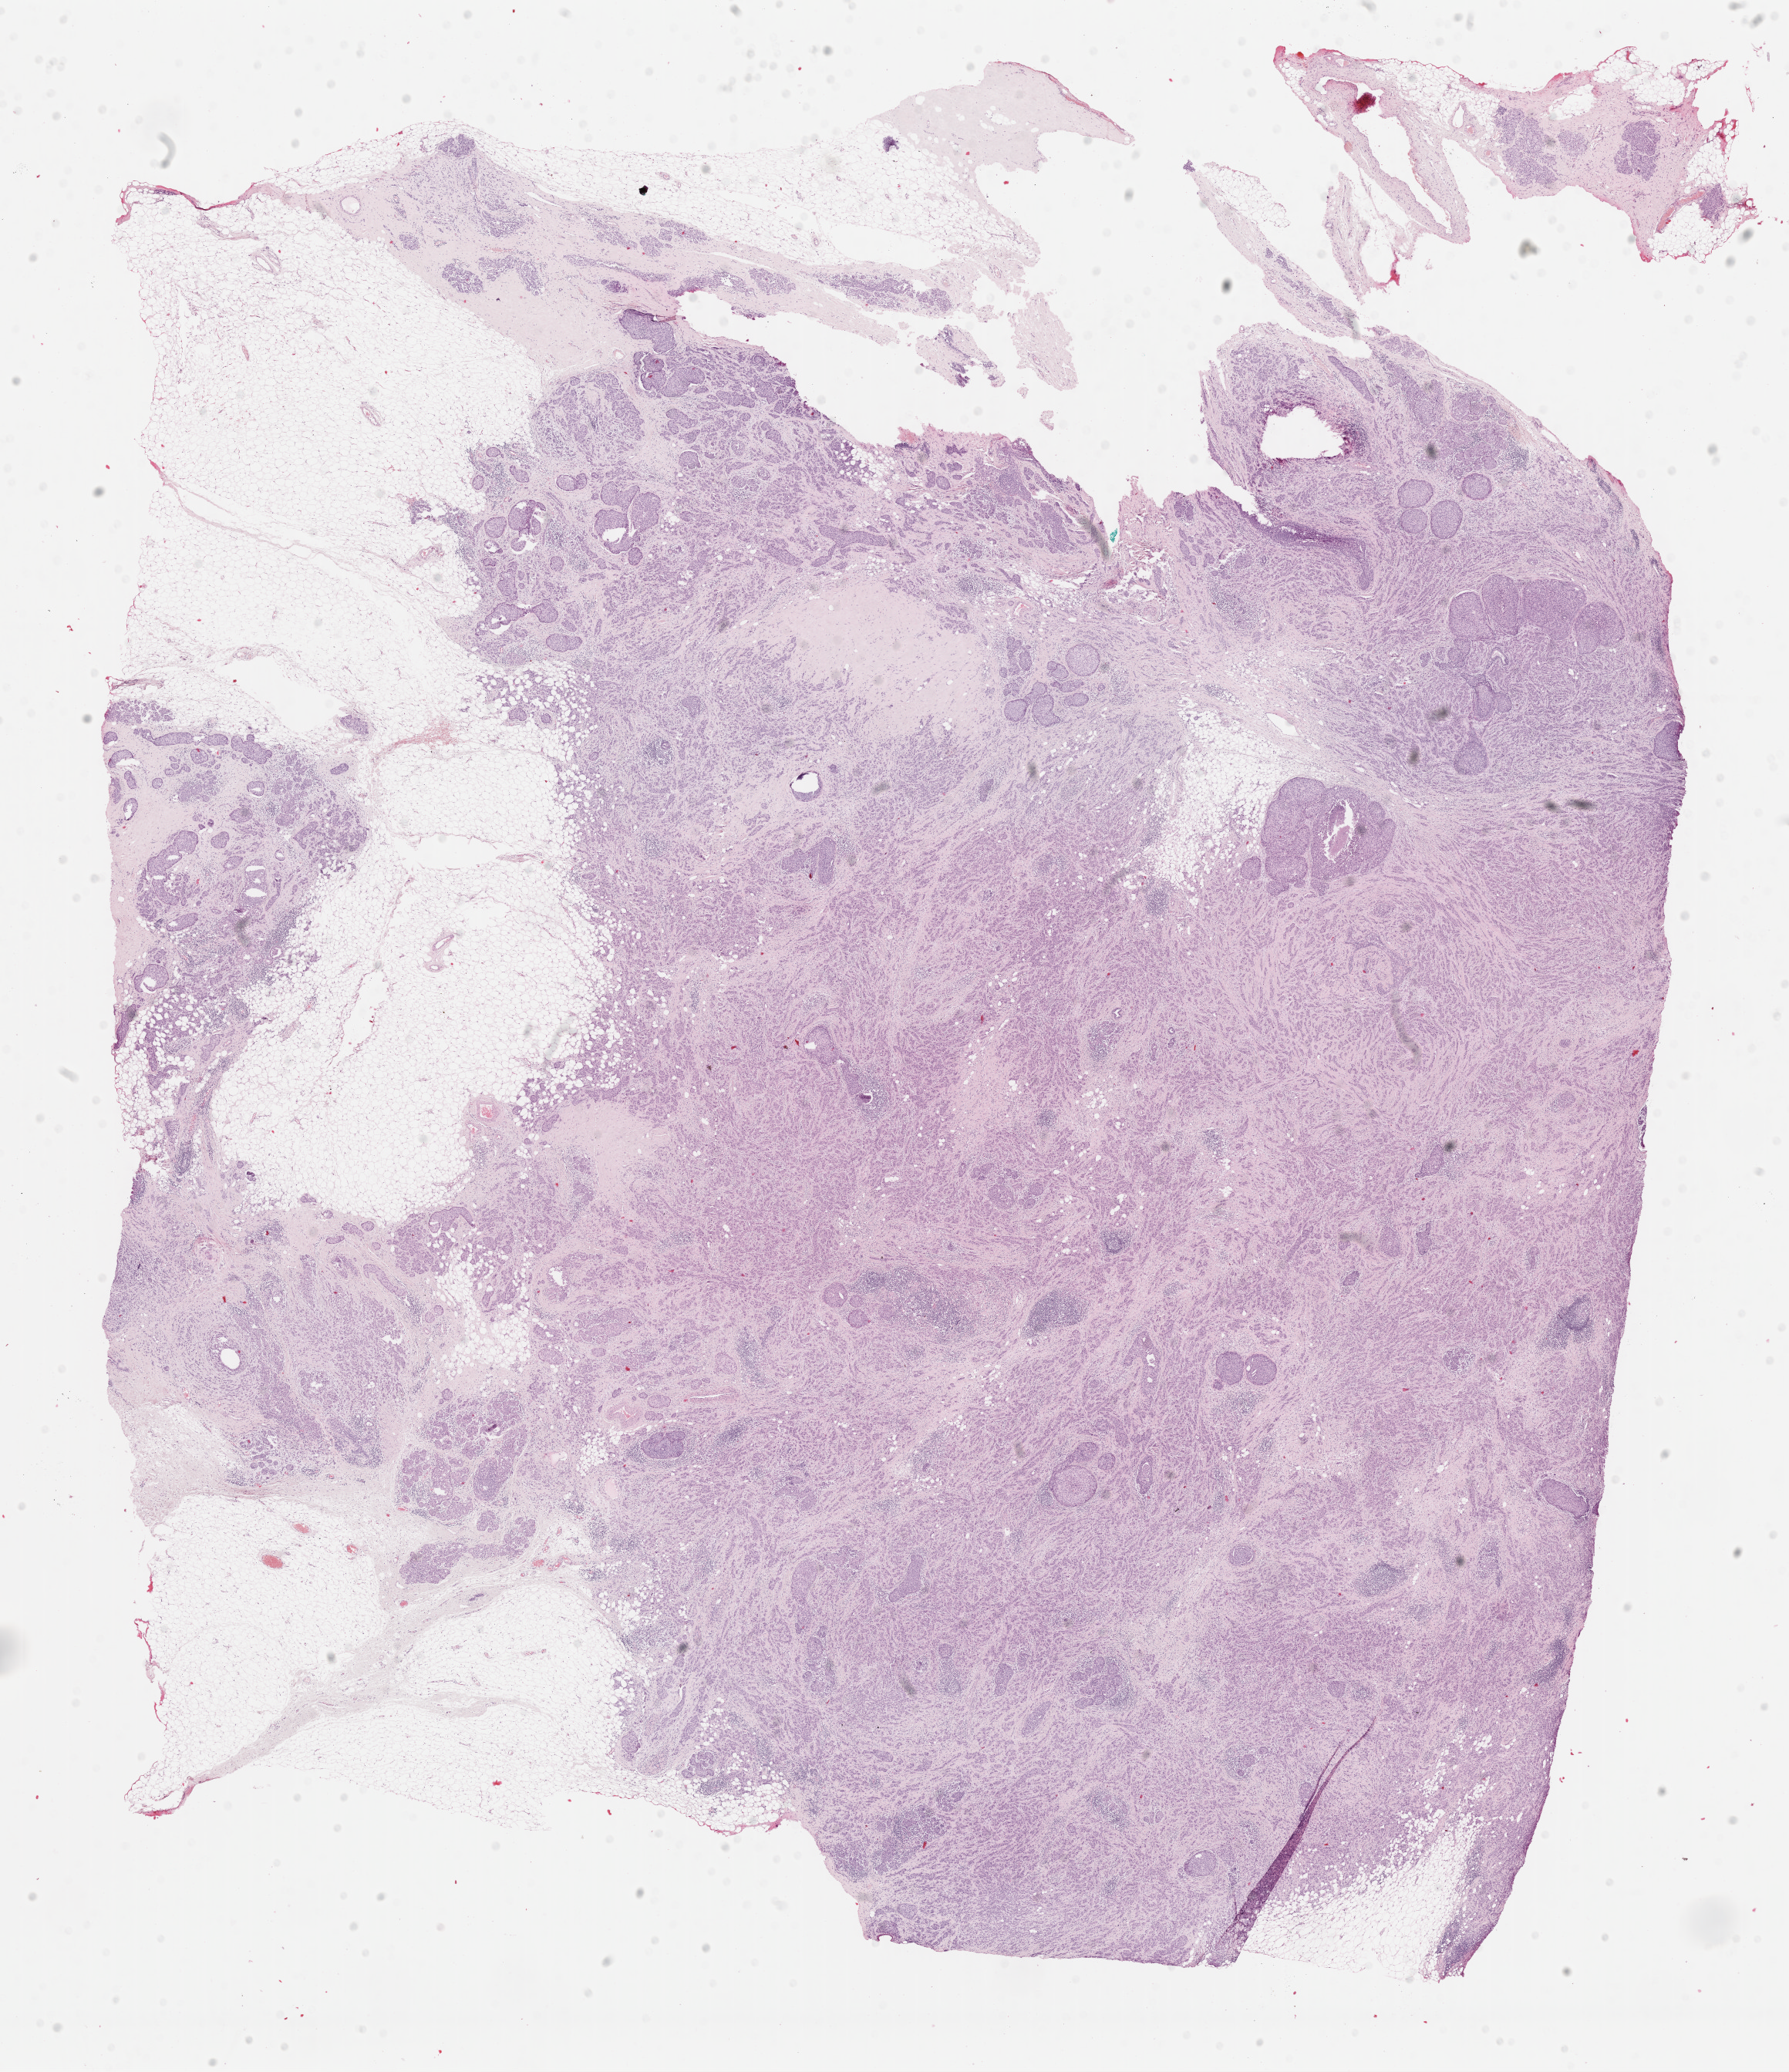
Digitized Hematoxylin and eosin (H&E) stained tissue section (whole slide) — a low-resolution overview of the entire scanned area, about 18.3 x 21.2 mm (acquisition: 40x scan), FFPE section, sample: primary tumour, breast. Female, age 47 years at initial diagnosis.
• lymph nodes positive (case pathology): 2 of 17 examined
• TNM: T2 N1a M0
• histologic diagnosis: Infiltrating duct carcinoma, NOS
• AJCC pathologic stage: IIB